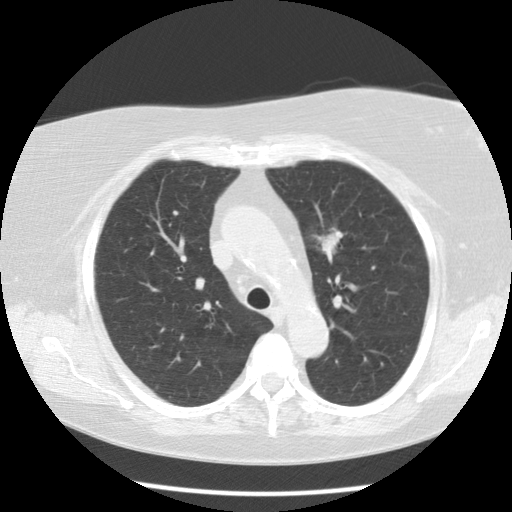
Chest CT (low-dose screening protocol), one axial image; second screening round (one year after baseline); lung window (W 1500 / L -600 HU); 2.5 mm slice thickness; standard (soft-tissue) reconstruction kernel (STANDARD); slice 28 of 109 in the series; 512 × 512 image matrix. Female participant, aged 67 years at enrolment.
Expert-annotated lung lesion, bounding box <292,215,353,269> (left, top, right, bottom; pixels). Reader record for this screening exam (exam-level; its link to the box is not recorded): non-calcified nodule or mass ≥4 mm, left upper lobe, 20 × 18 mm, poorly defined margins, soft tissue attenuation, pre-existing on the prior screen: yes; interval growth: yes. Participant outcome: lung cancer diagnosed 28 days after this screen — adenocarcinoma, NOS, left upper lobe, moderately differentiated (G2), stage IIA (AJCC 6th edition), 23 mm at pathology.